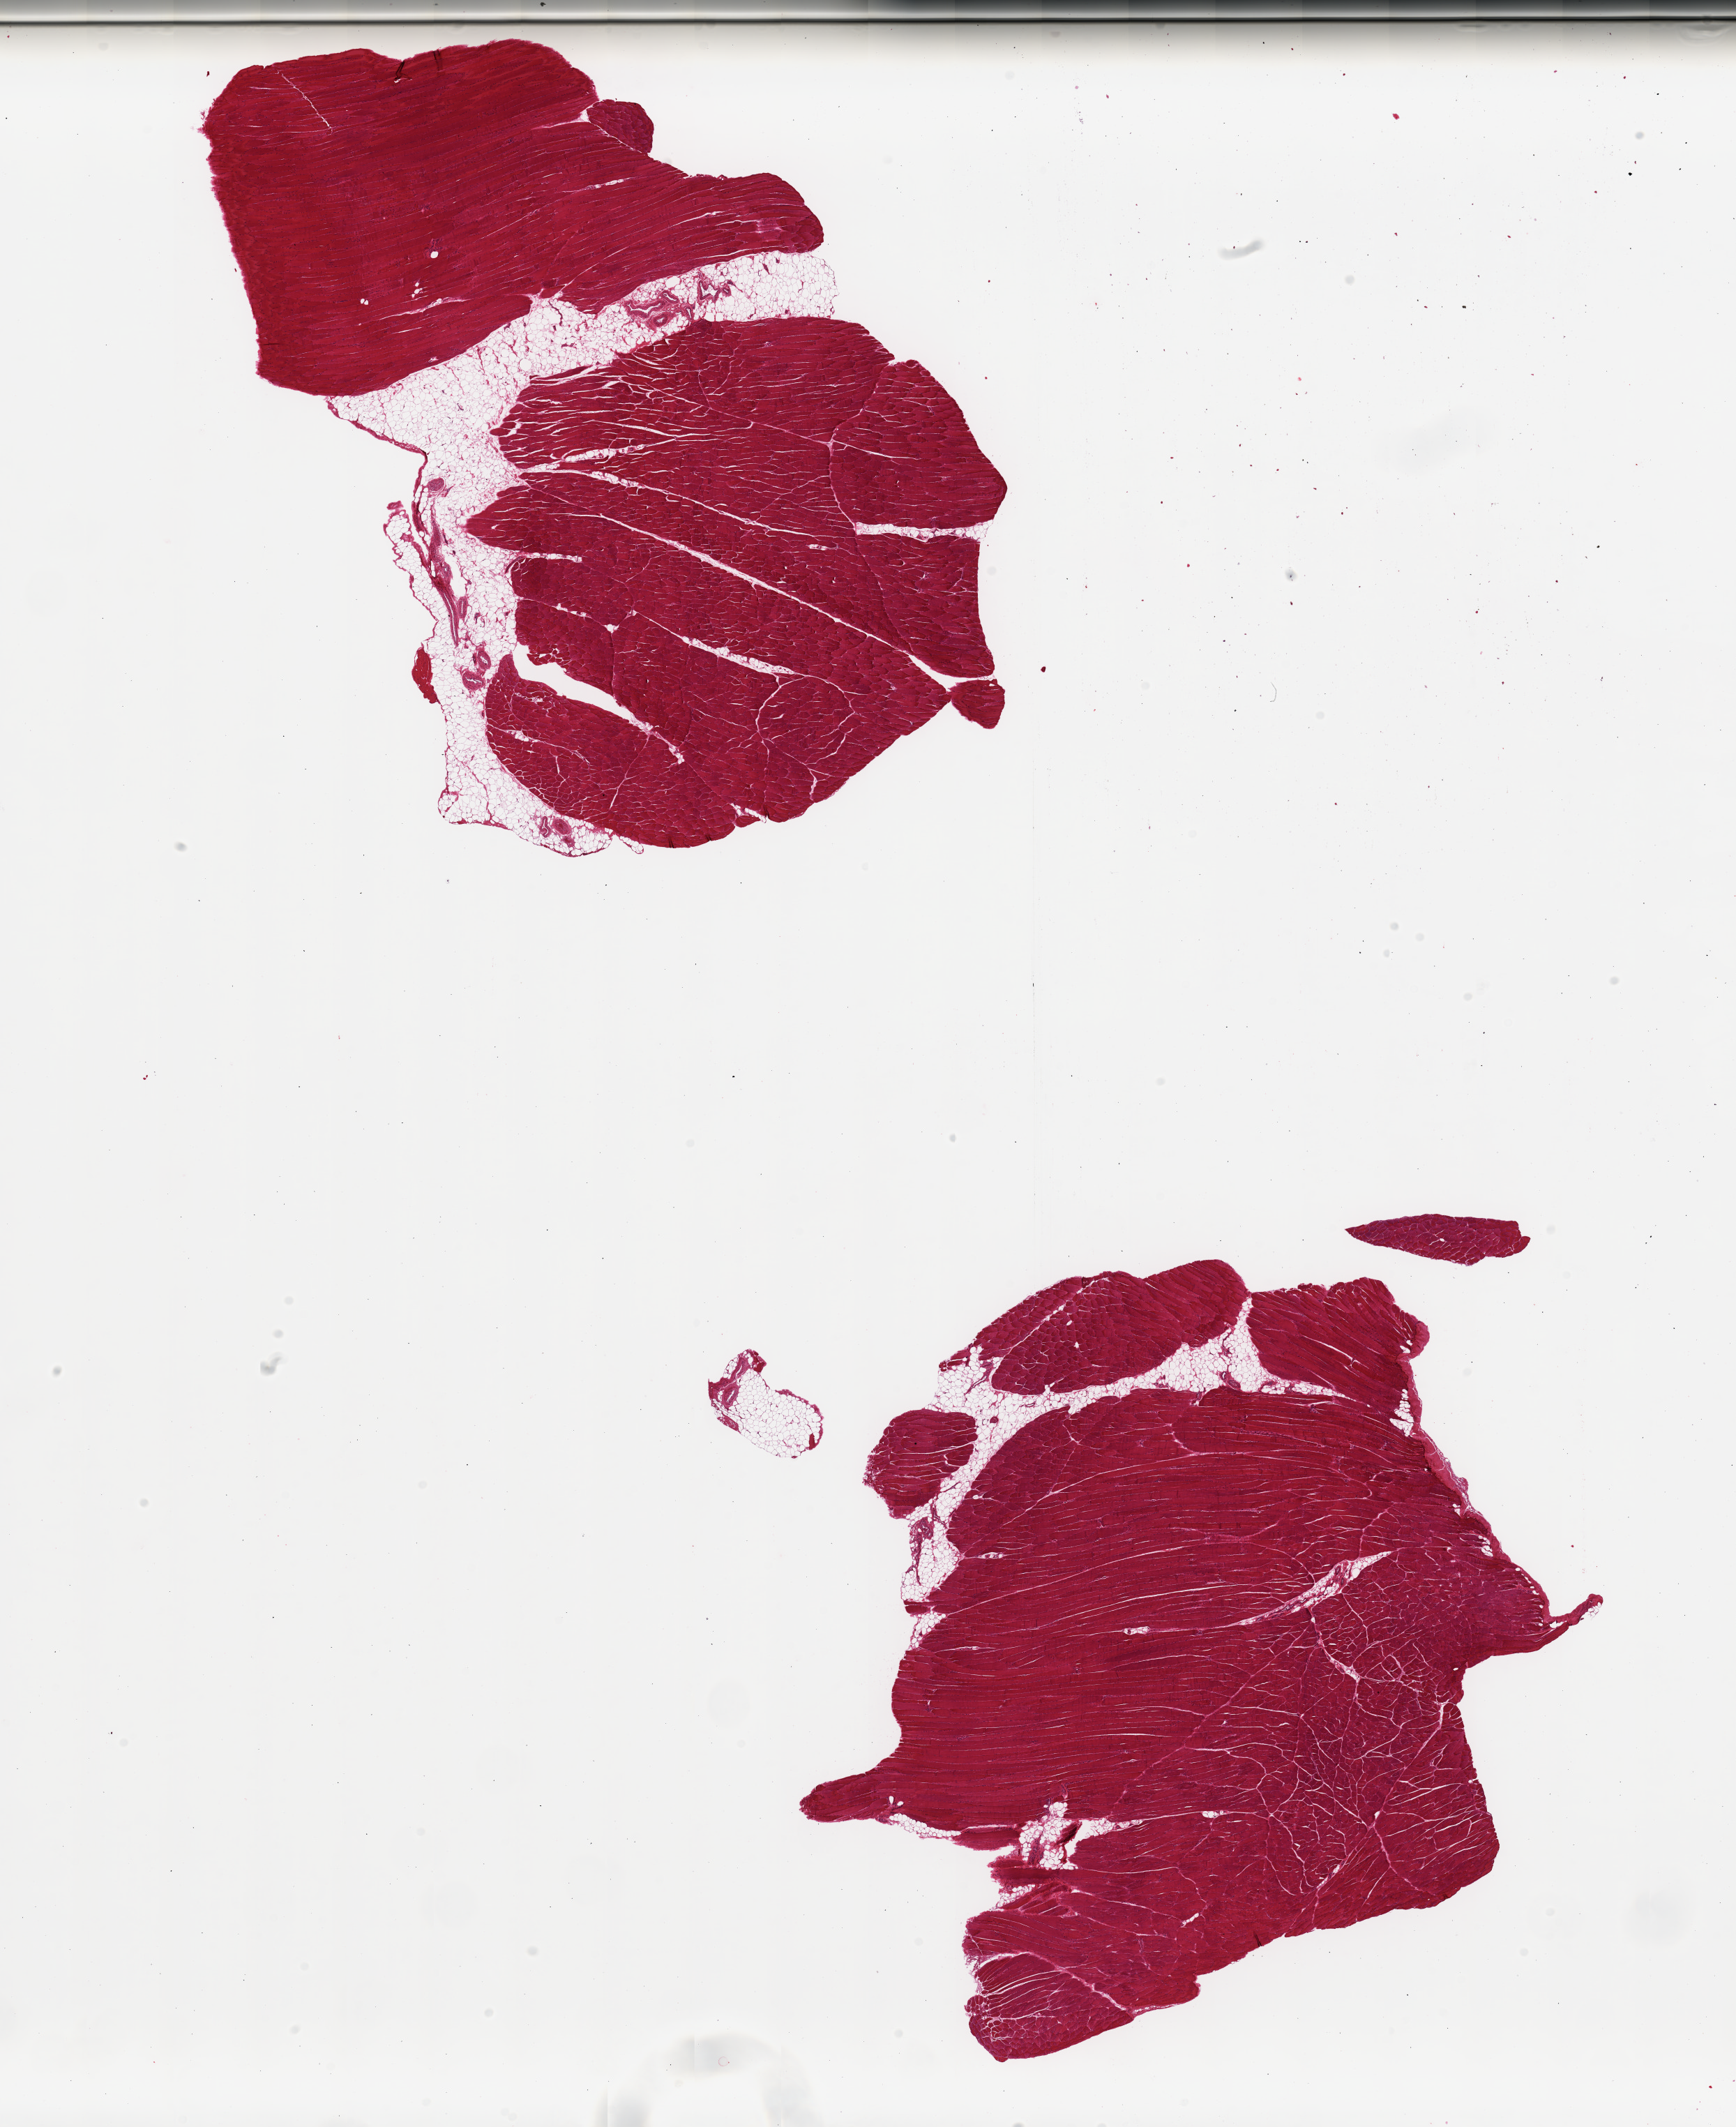
H&E whole-slide image, whole scanned area (about 19.7 x 24.1 mm) shown as a low-resolution overview; PAXgene-fixed paraffin-embedded (PFPE) section; target tissue: skeletal muscle; tissue donor sample. Female donor.
Review note (as recorded): 2 pieces, ~15% interstitial fat/vascular elements.